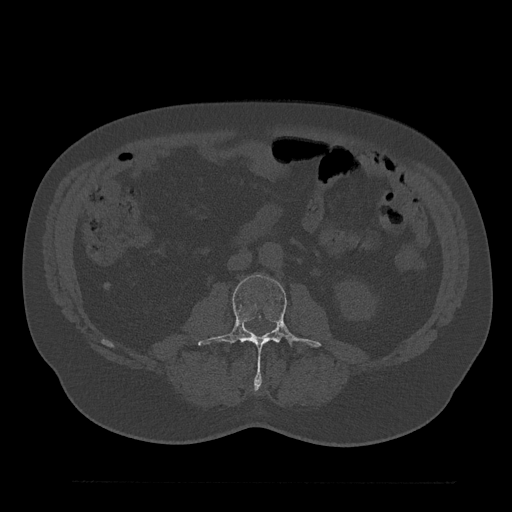
CT including the spine, one axial slice. Position 36 of 797 along the scan axis. Reconstruction kernel Br40s/3. Bone window (W 1800 / L 400 HU). 0.5 mm slice thickness. 512 × 512 image matrix, field of view 430 × 430 mm. Patient: male, 61 years. Case-level facts recorded for this patient, not image findings: primary cancer: prostate.
Outlined on this slice (semi-automatically segmented with operator editing):
- L3 vertebra: box from (x=198, y=274) to (x=321, y=388) px